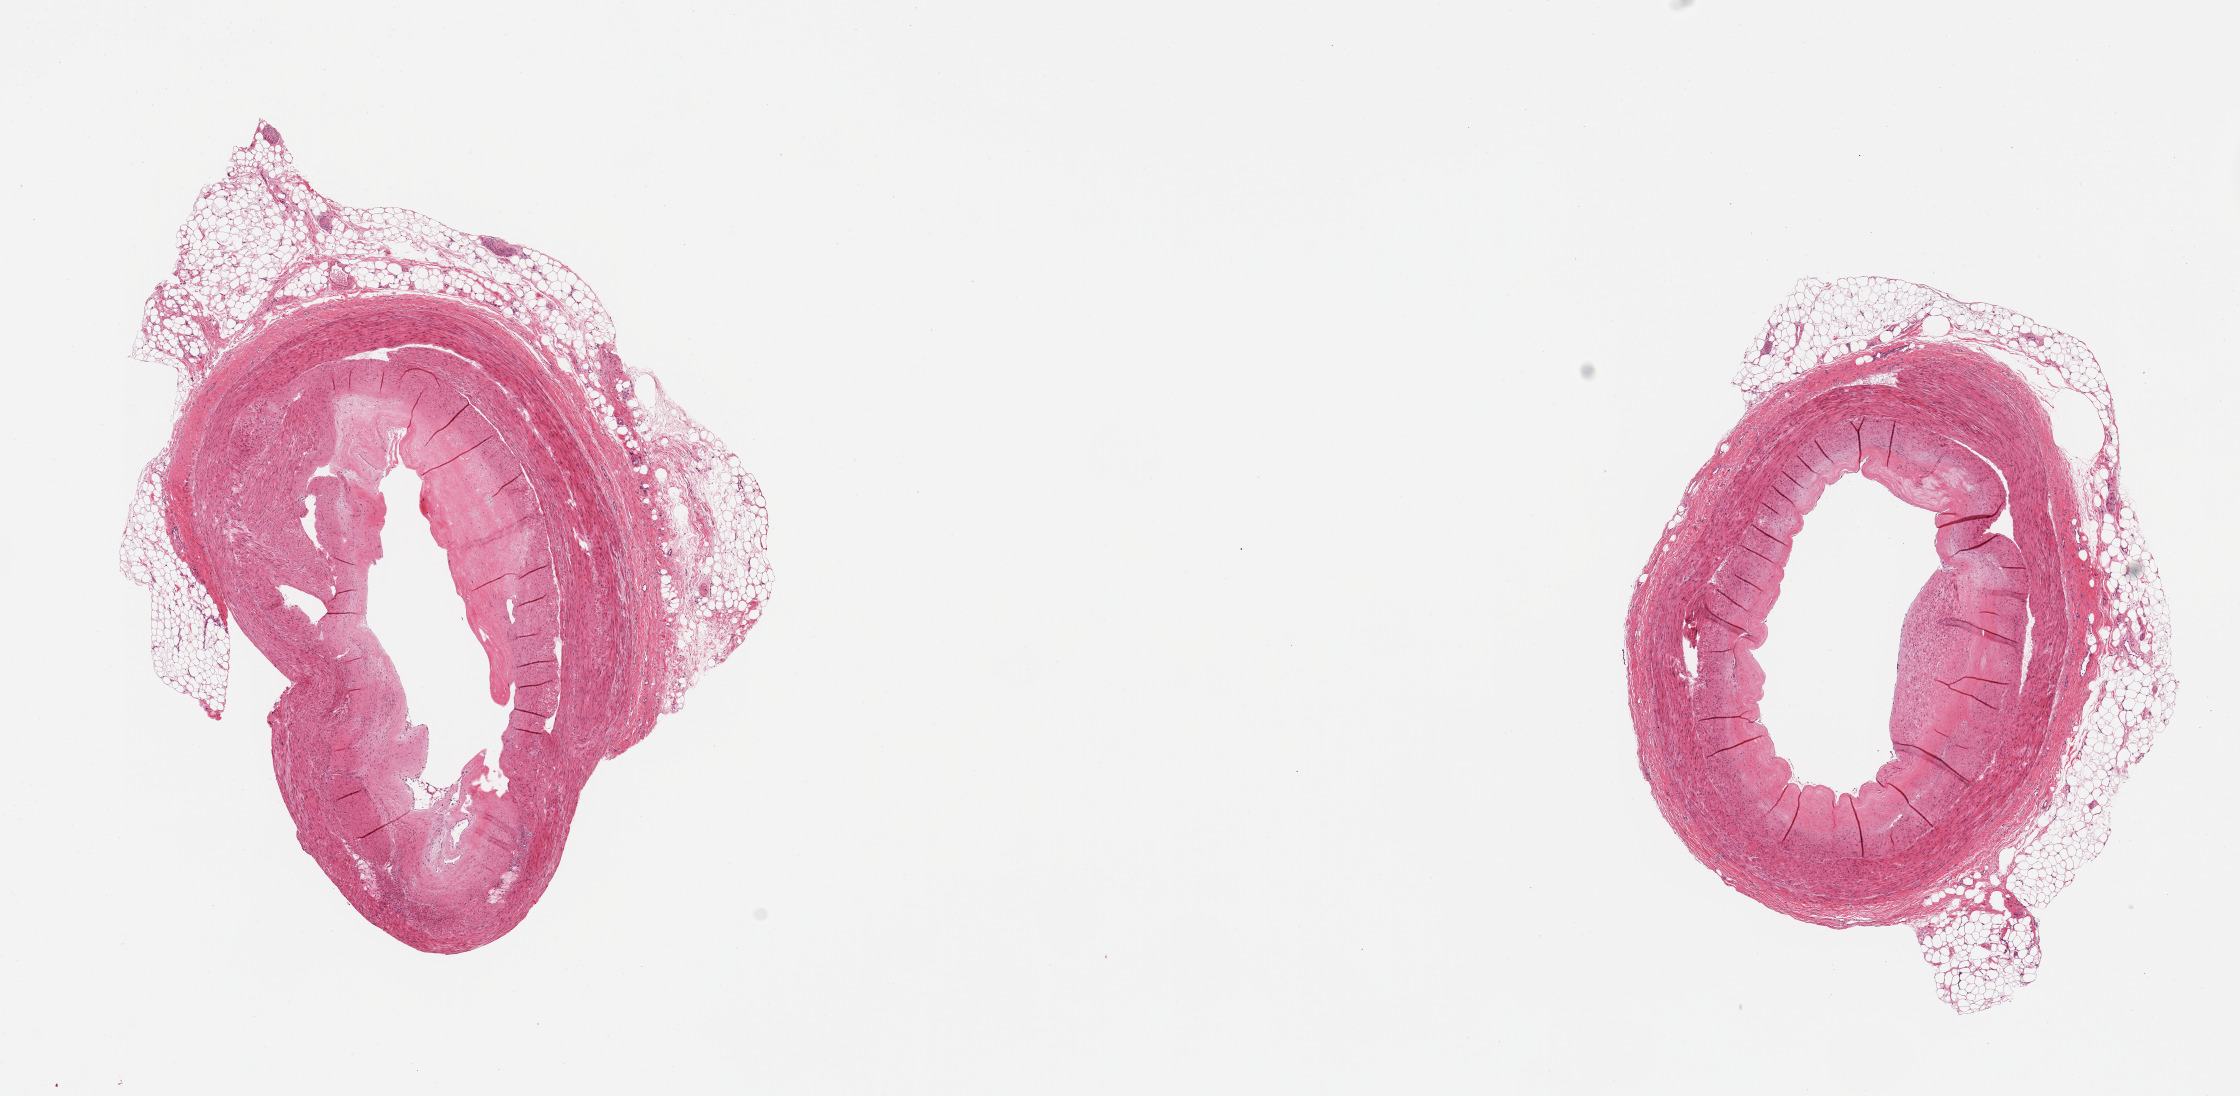
Digitized hematoxylin and eosin (H&E)-stained section — a low-resolution overview of the entire scanned area, about 17.7 x 8.7 mm (from a 20x scan); PAXgene-fixed paraffin-embedded (PFPE) section; target tissue: coronary artery; tissue donor sample.
Pathologist's review note for this sample: 2 pieces; eccentric fibrosclerotic plaque with 50% luminal compromise; up to 1 mm external fat on each.